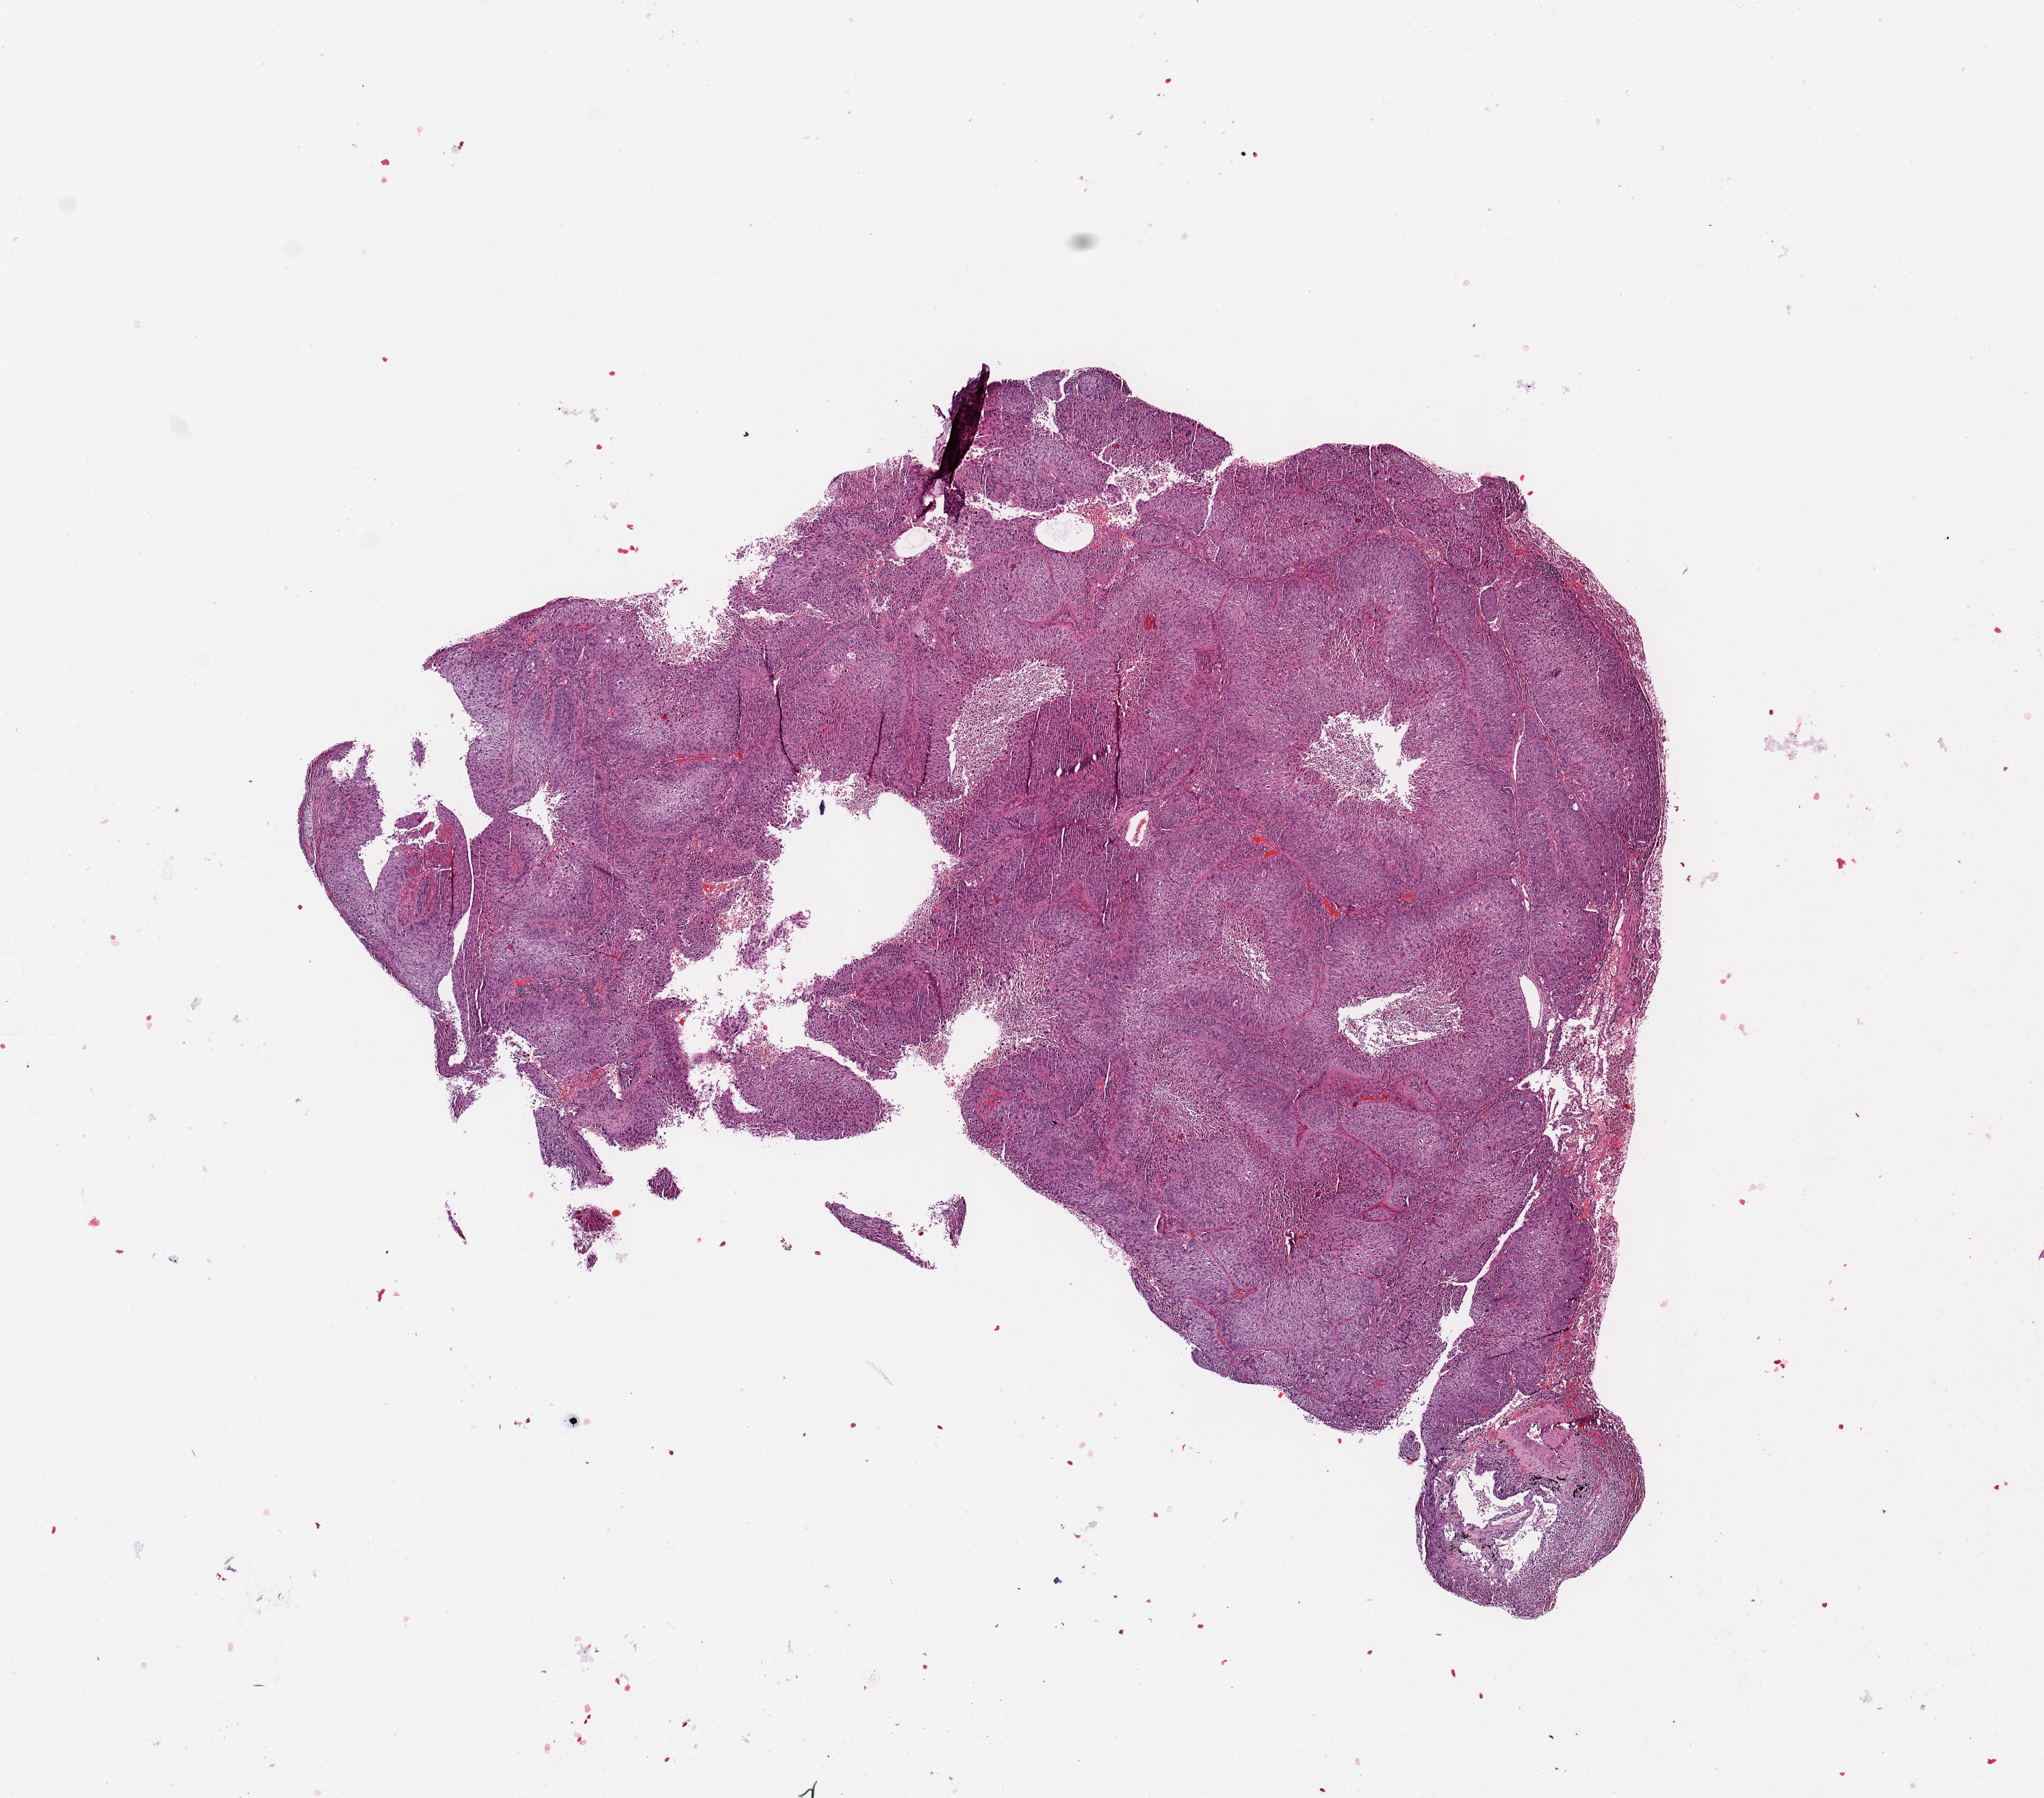
H&E-stained whole-slide image, low-resolution overview of the scanned area, about 11.8 x 10.4 mm. Lung, tumour tissue. 64-year-old female patient. Histologic grade: G3 (poorly differentiated).
• primary tumour site (as recorded): right lower lobe
• diagnosis: Squamous cell carcinoma, NOS
• AJCC pathologic stage: IA